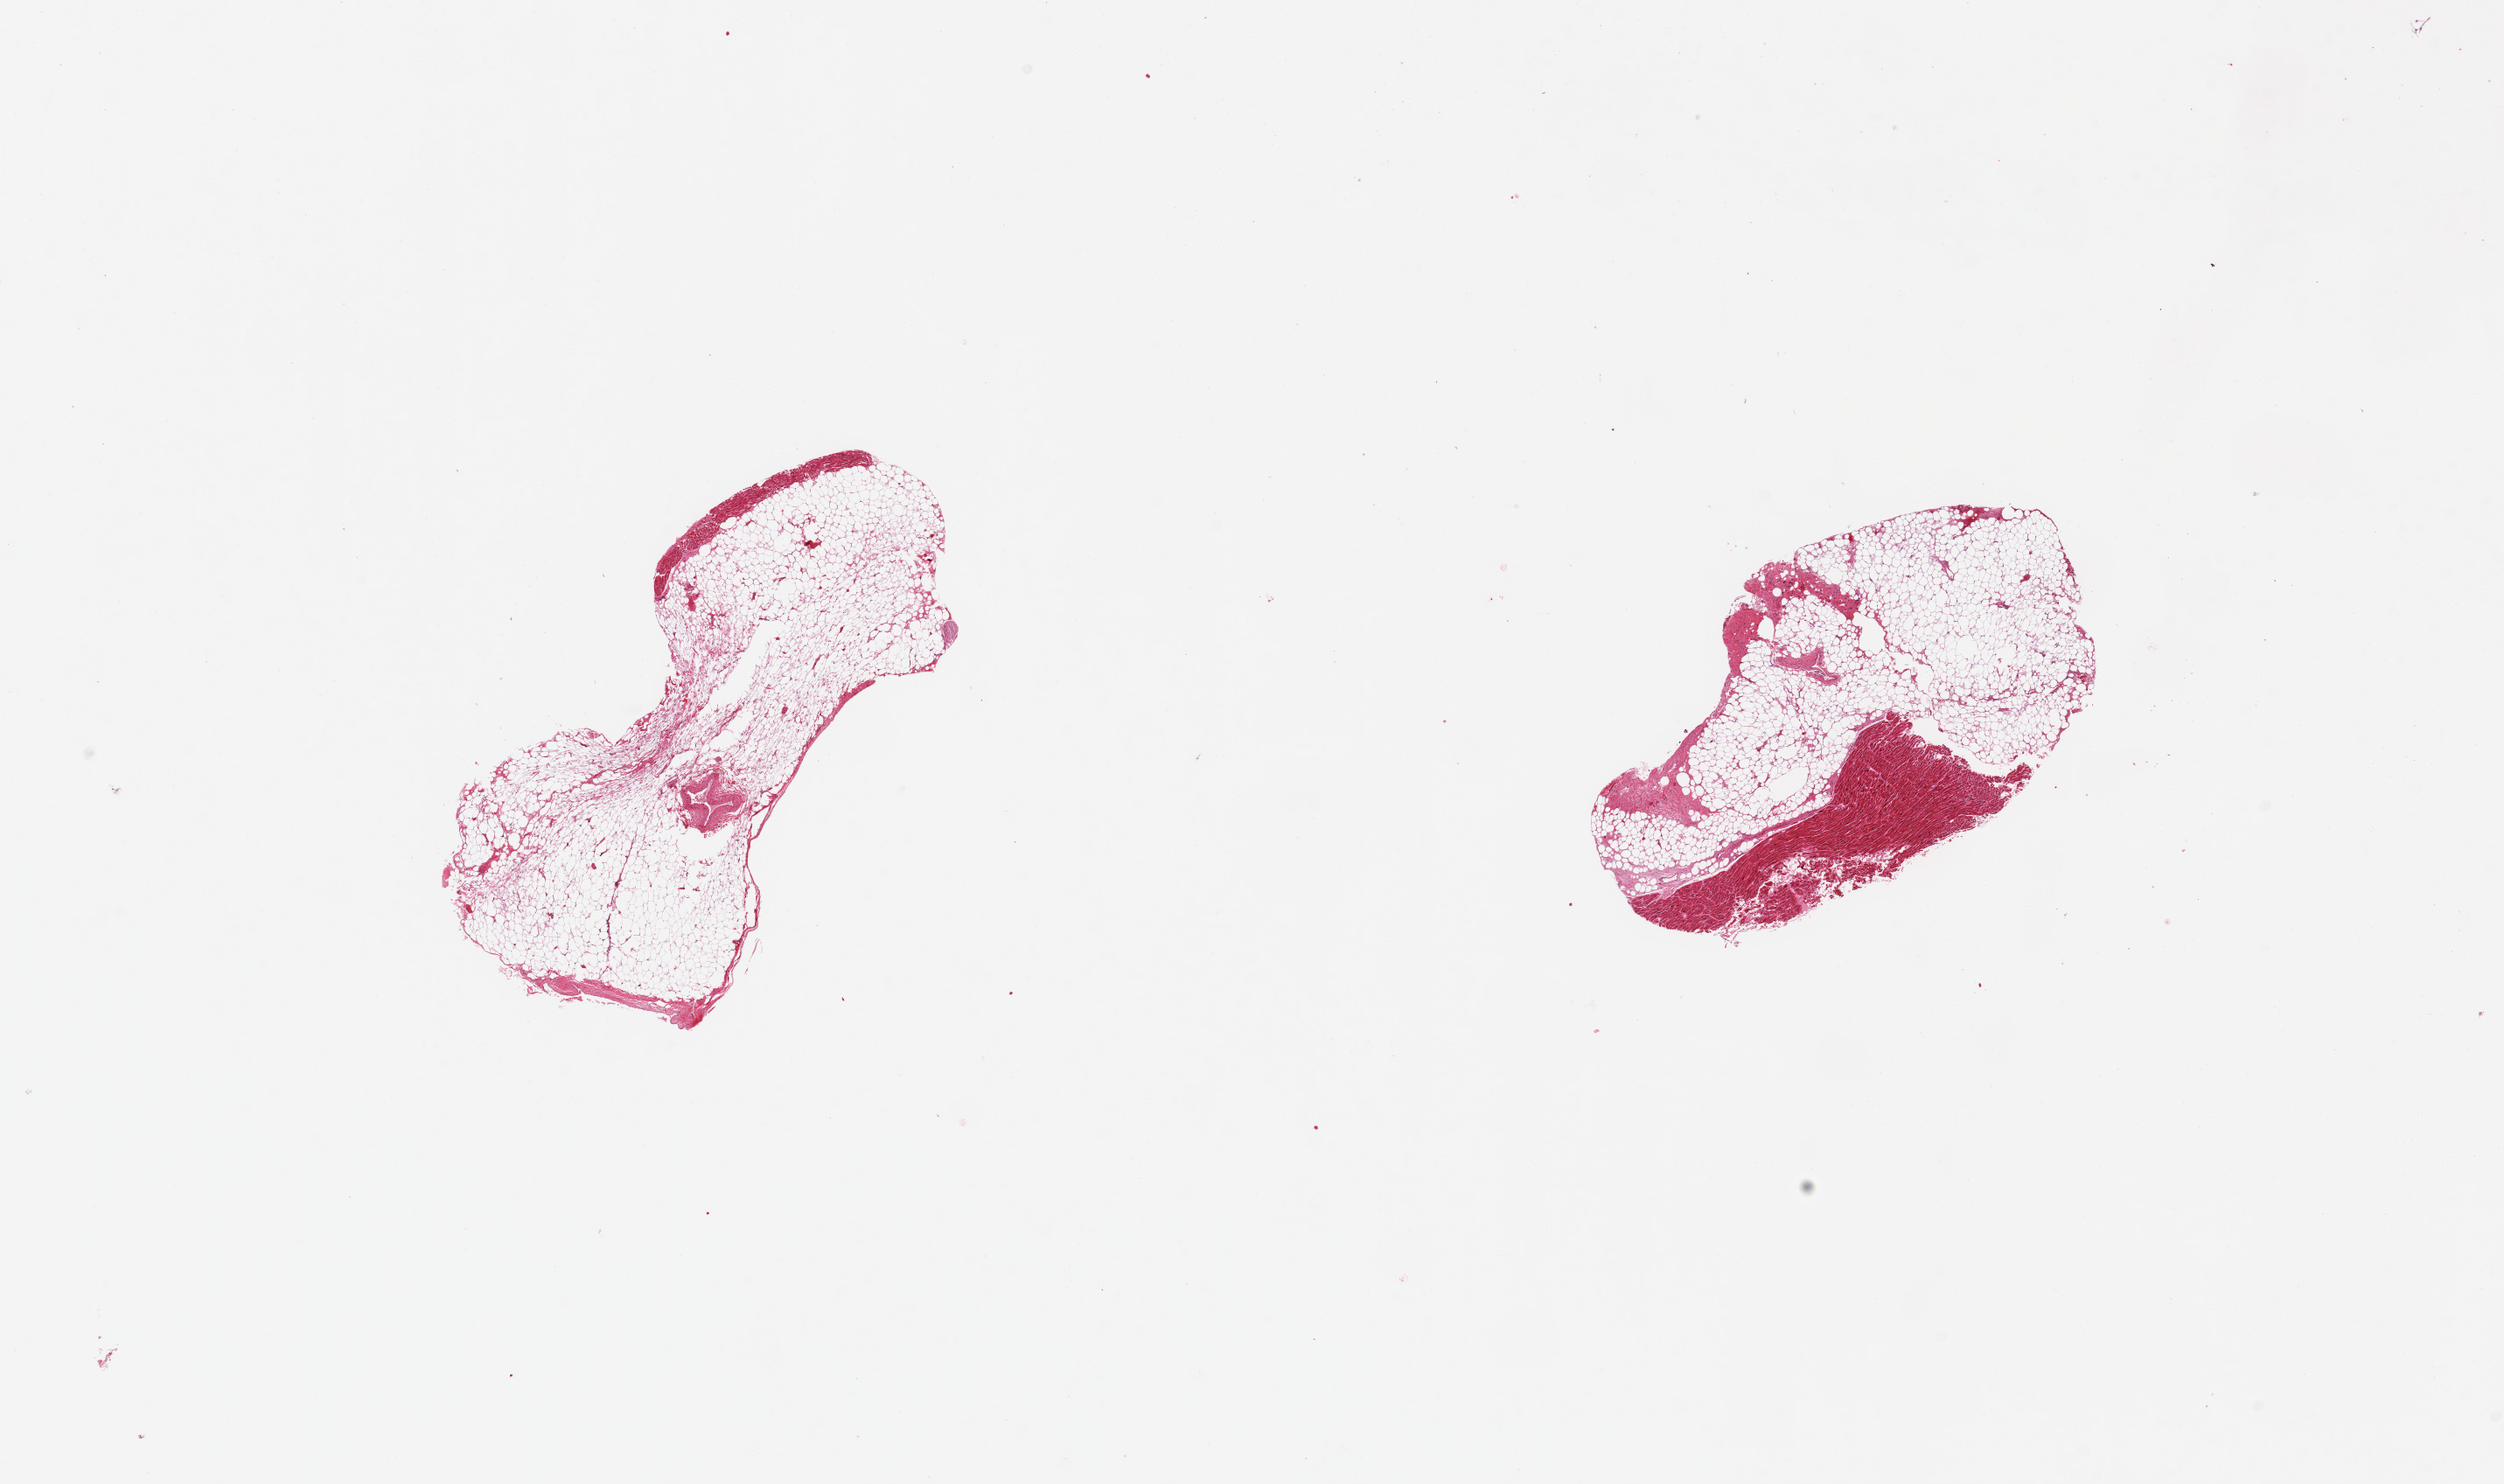
Digitized H&E-stained section, brightfield — low-resolution overview of the scanned area, about 22.6 x 13.4 mm, PAXgene-fixed paraffin-embedded (PFPE) section, target tissue: coronary artery, tissue donor sample.
- reviewer comment on this tissue sample: 2 pieces; 1 with small vessel and over 90% fat; other is all fat and myocardium